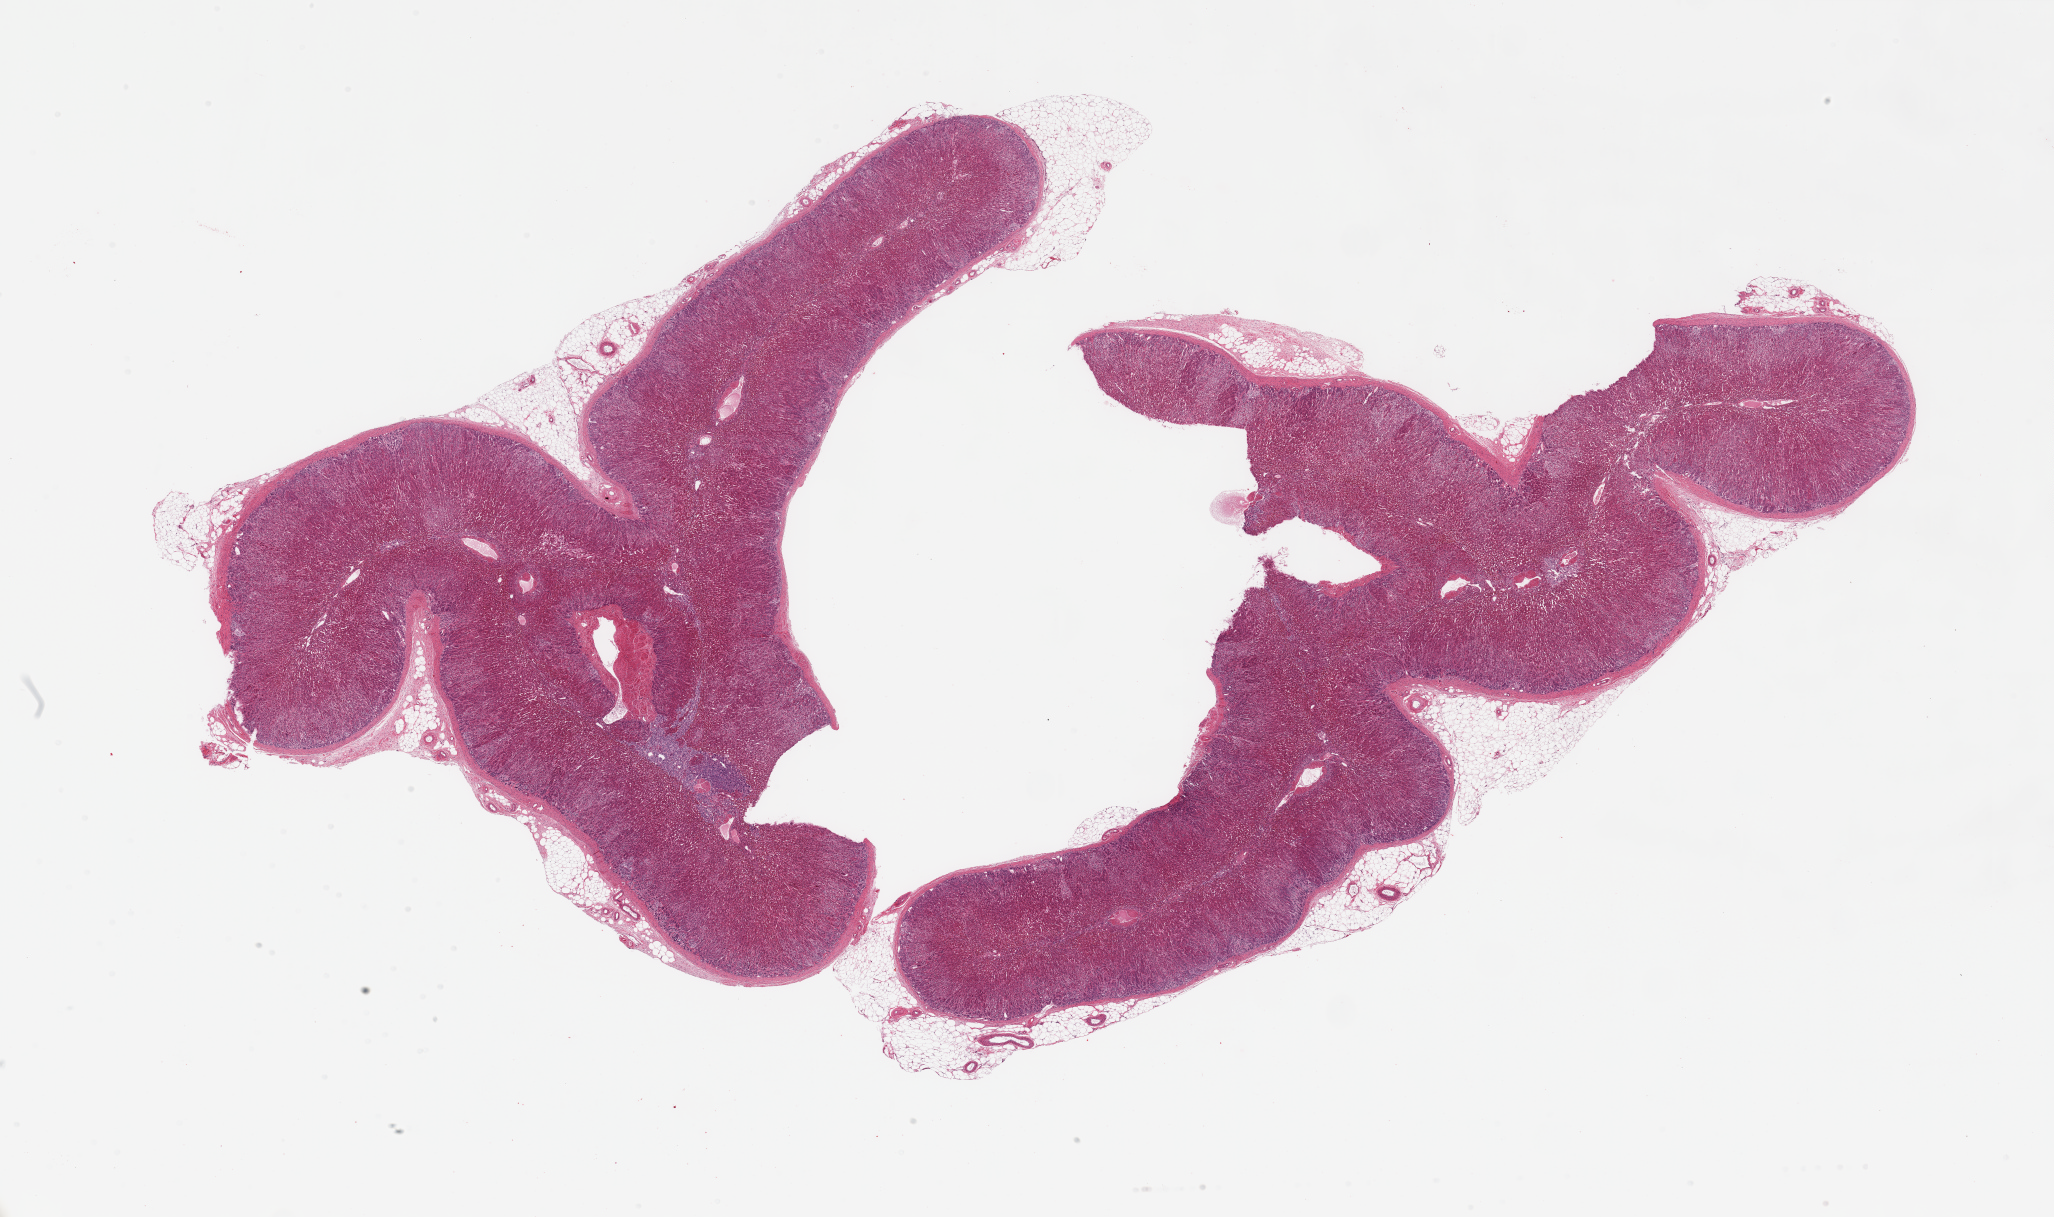
Whole-slide image, hematoxylin and eosin (H&E) stain — shown as a low-resolution overview of the whole scanned area (about 32.5 x 19.2 mm). PAXgene-fixed paraffin-embedded (PFPE) section. Sampled site (target tissue): adrenal gland. Tissue donor sample. Male donor.
• reviewer comment on this tissue sample: 2 pieces, all cortex, few adherent fat nubbins up to ~2.5mm